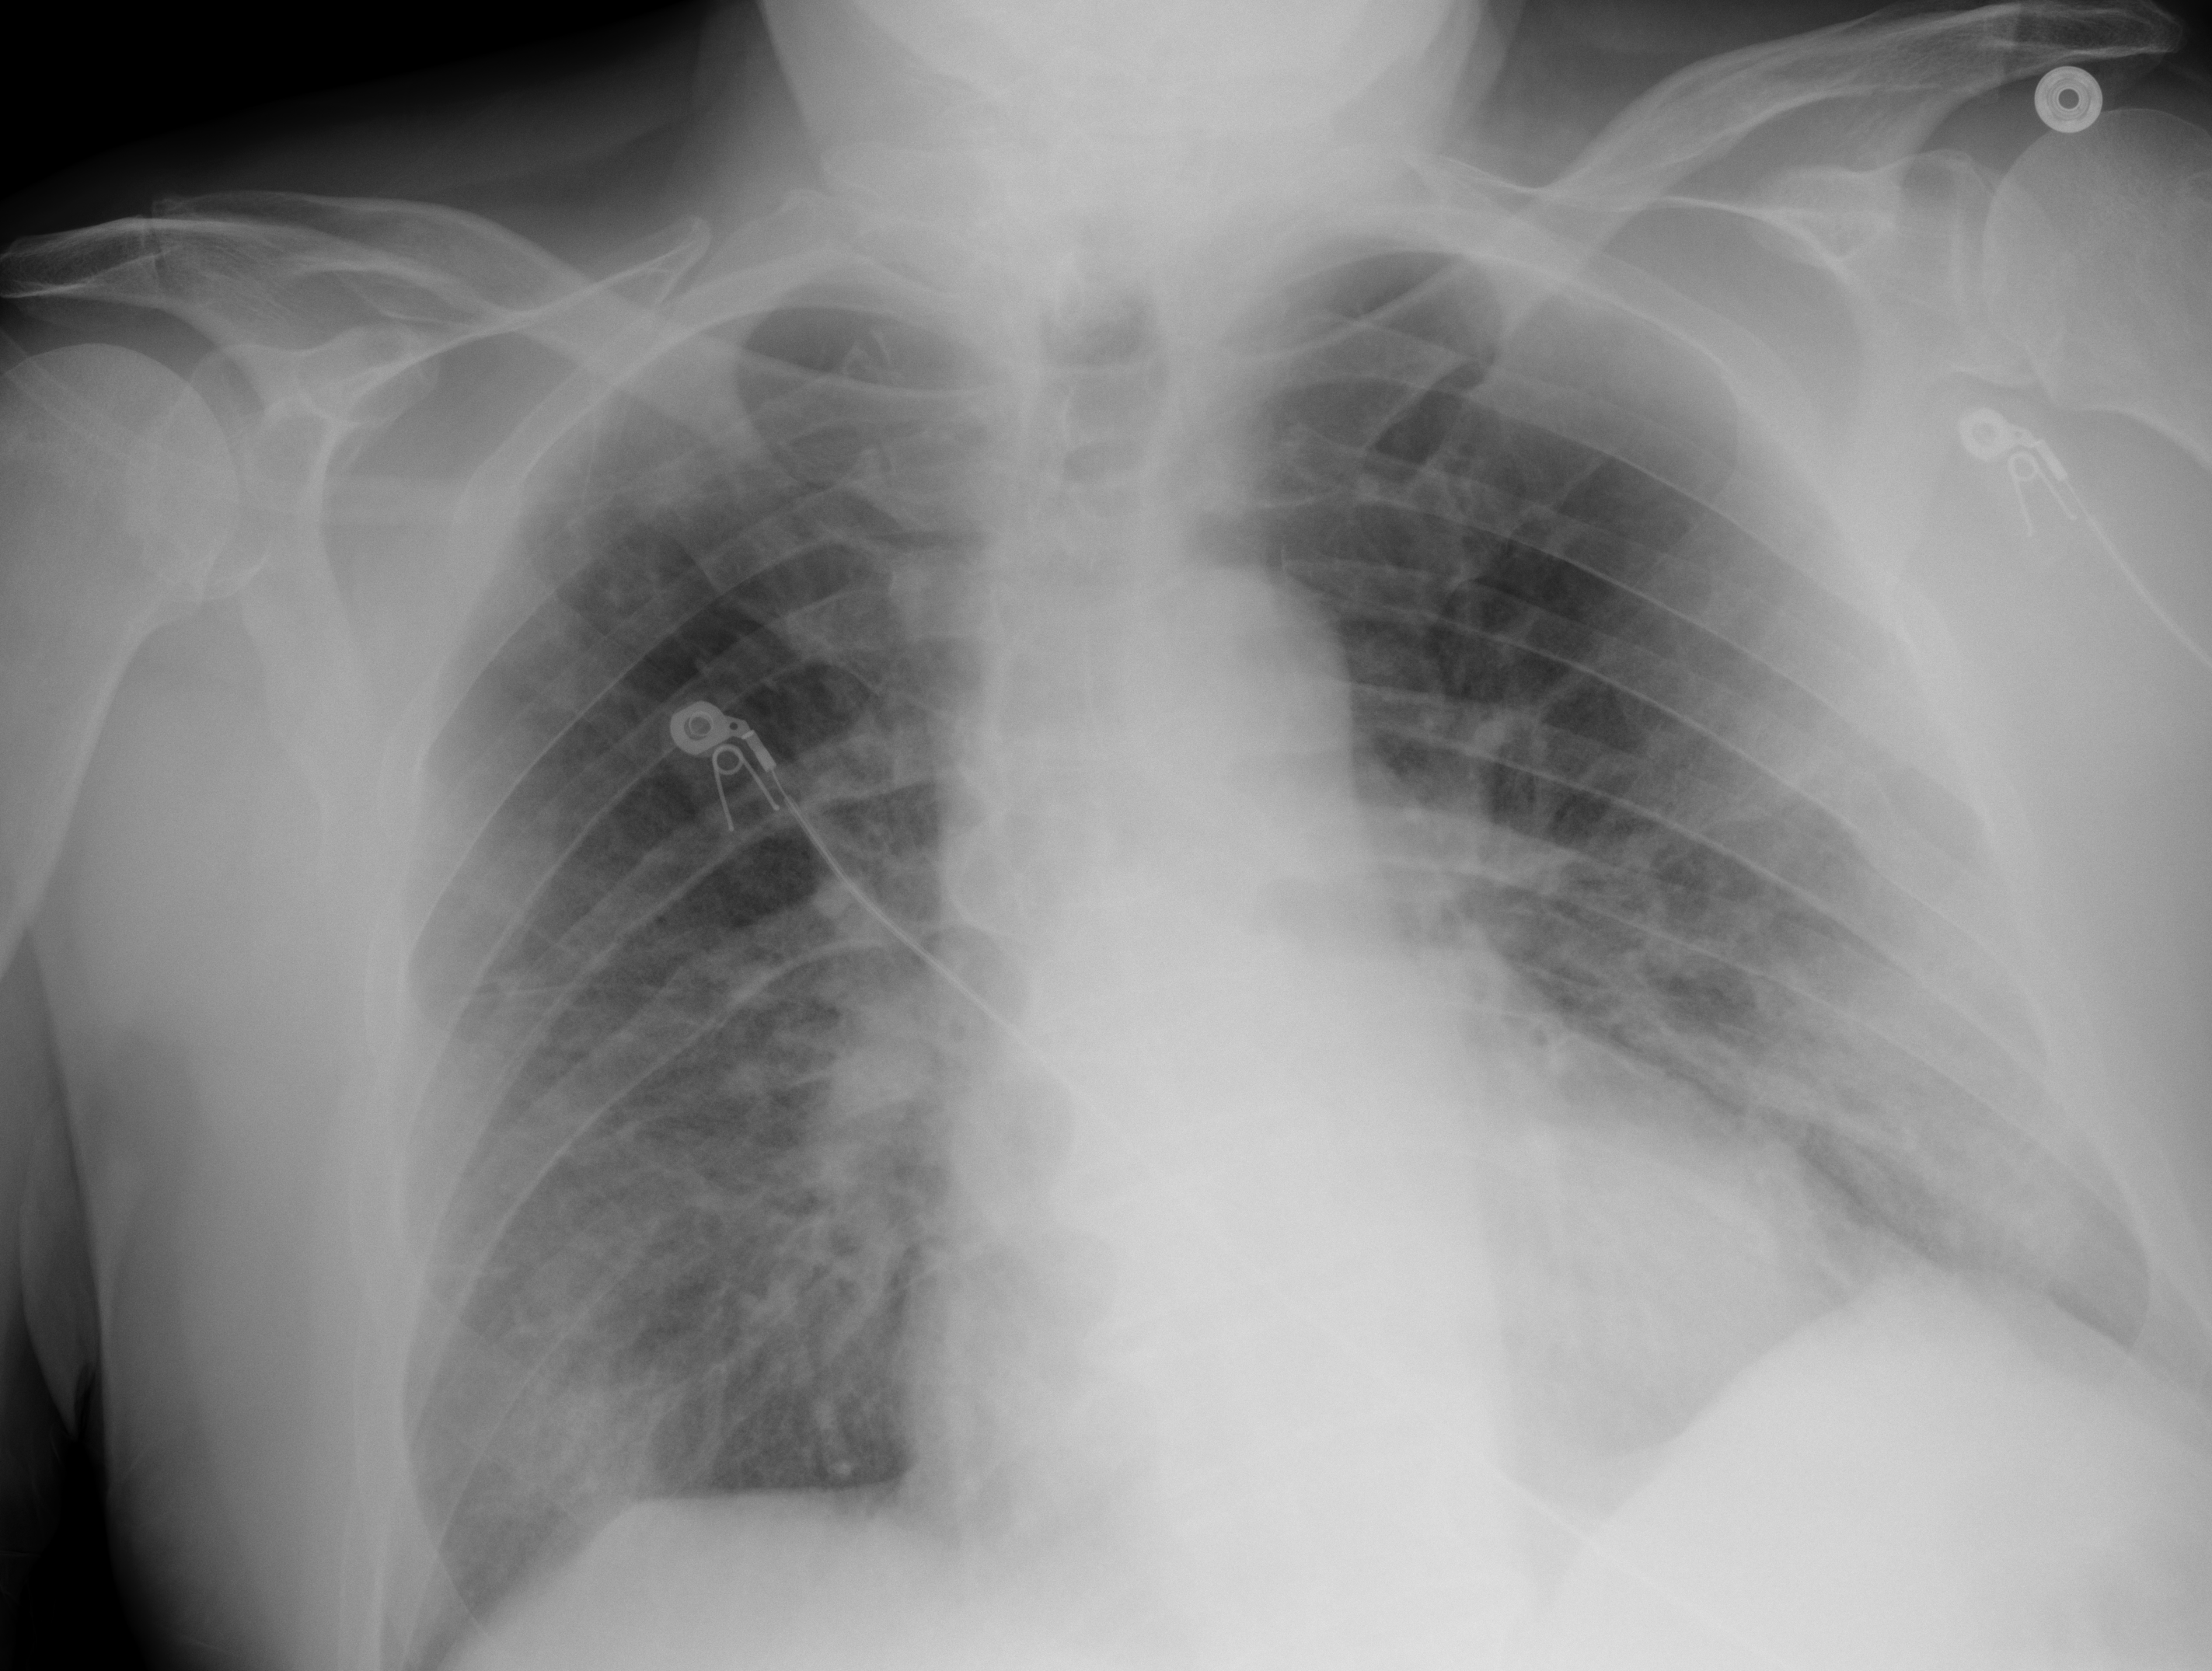
Chest X-ray (portable), AP projection. Male patient, age 79 years; imaged 0 days after the COVID-19 diagnosis.
Radiologist's key findings for this exam: No focal airspace consolidation or pleural effusion.